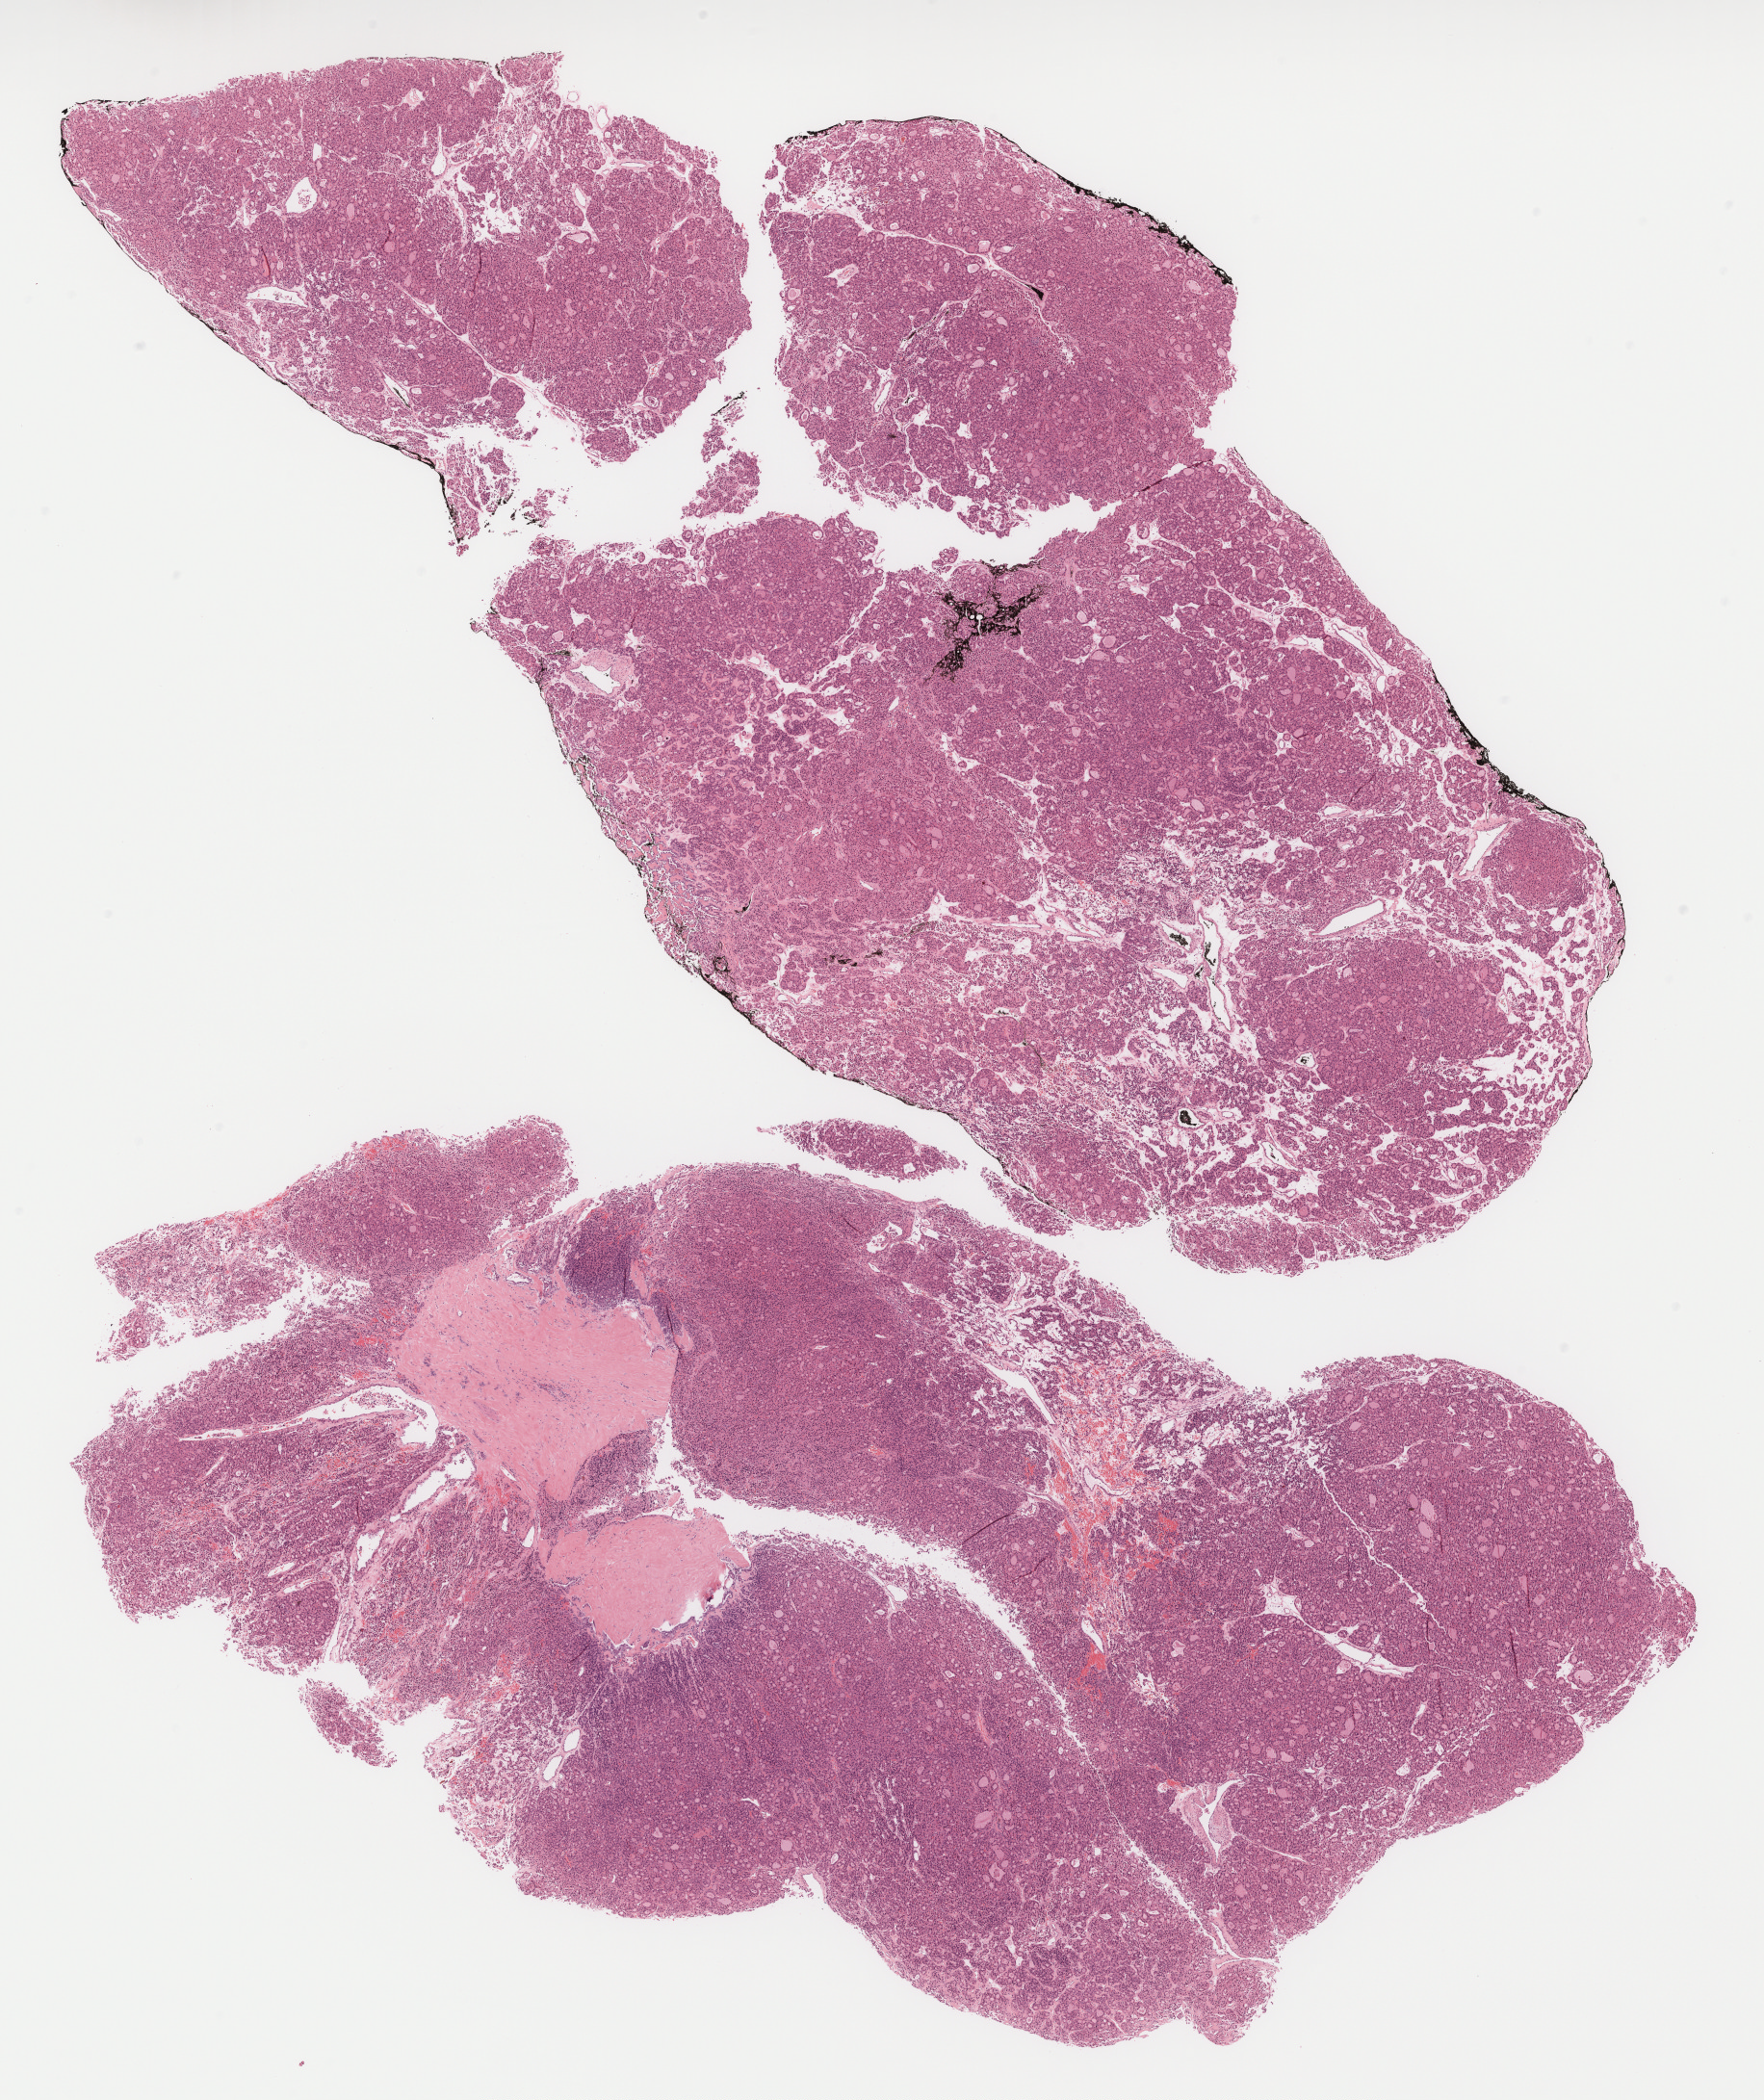
Whole-slide histology image, H&E-stained, whole scanned area (about 14.8 x 17.6 mm) shown as a low-resolution overview, formalin-fixed paraffin-embedded (FFPE) diagnostic section, thyroid, primary tumour sample. Female patient; age at initial diagnosis 46 years.
TNM: T2 N0 MX. Lymph nodes positive (case pathology): 0 of 1 examined. Laterality: right. AJCC pathologic stage: II (7th edition). Diagnosis: Papillary carcinoma, follicular variant (thyroid gland).